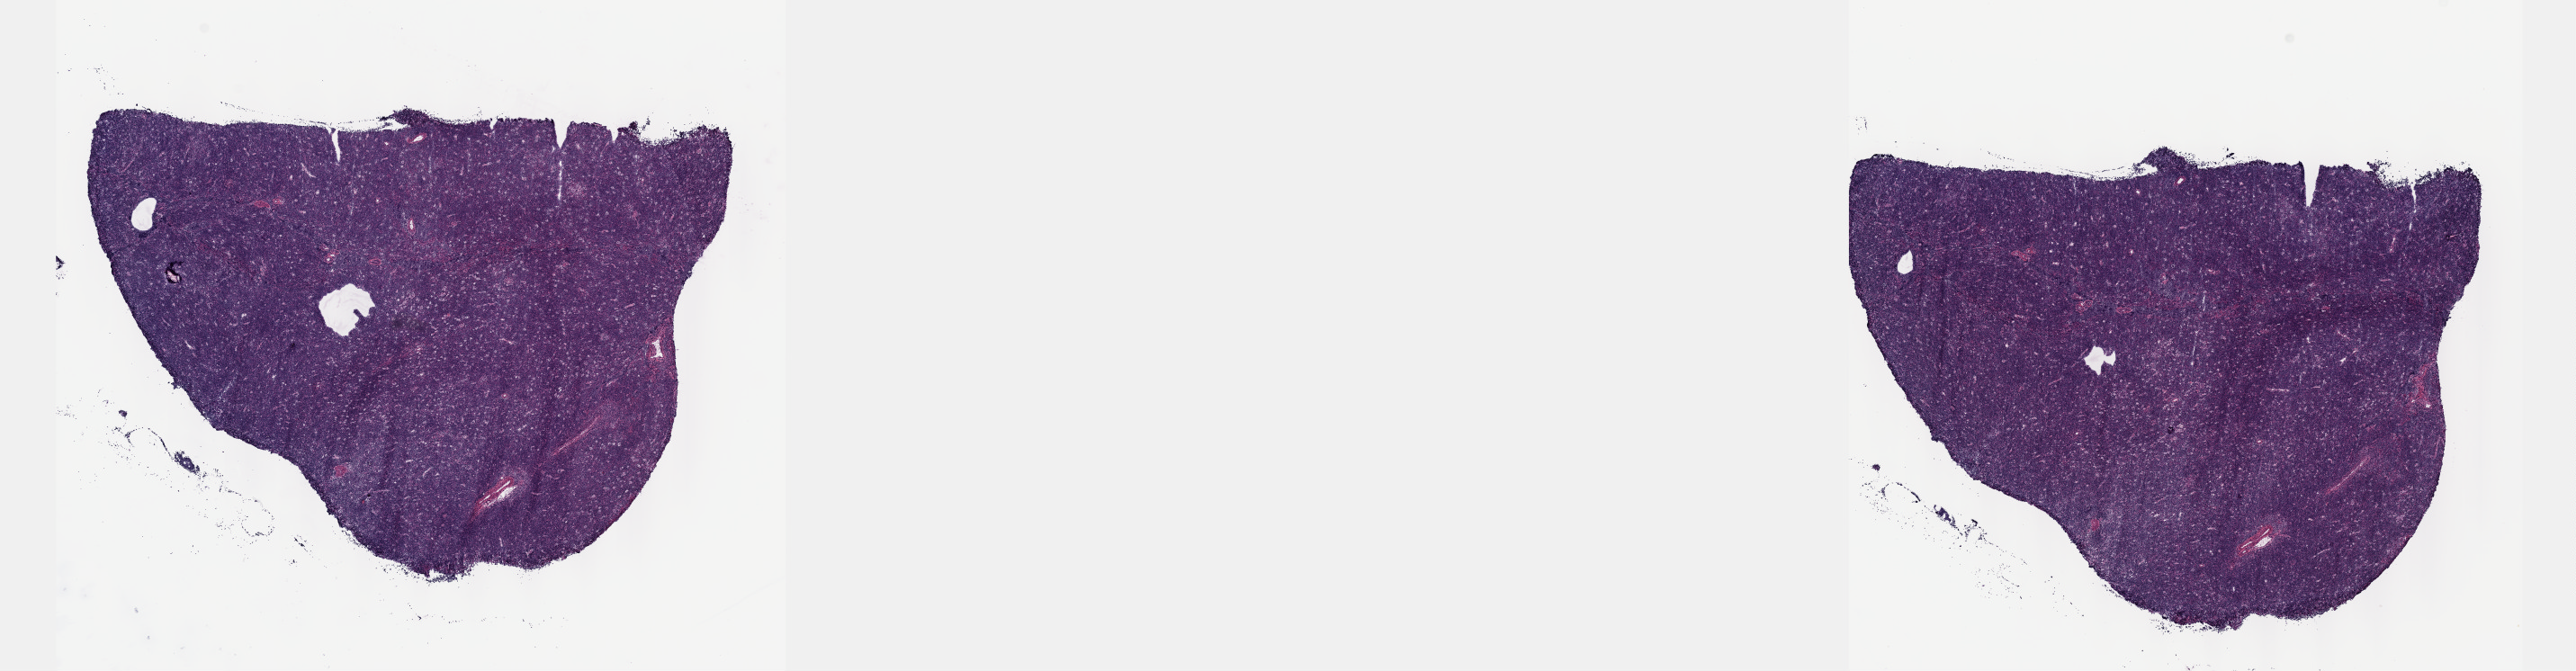
Hematoxylin and eosin (H&E) stained whole-slide image — whole scanned area (about 23.1 x 6.0 mm) shown as a low-resolution overview, frozen section from the top of the tissue portion, primary tumour sample from the thymus. Female, age 71 years at initial diagnosis. Pathologist review of this section (percent, as recorded): tumour cells 99%, tumour nuclei 99%, normal cells 0%, stromal cells 1%, necrosis 0%. Inflammatory infiltration, as recorded: lymphocyte infiltration 0%, monocyte infiltration 0%, neutrophil infiltration 0%.
- diagnosis: Thymoma, type B2, NOS